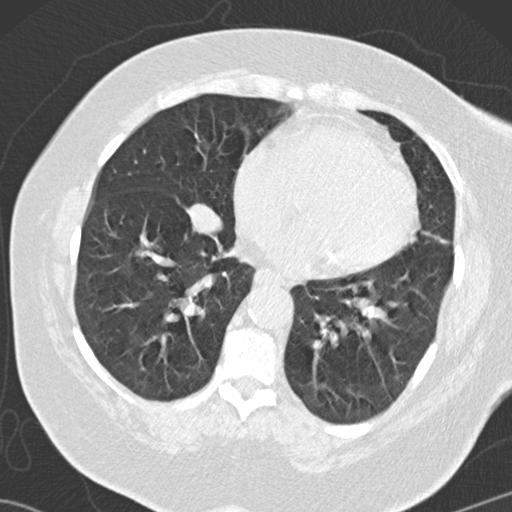
Low-dose screening chest CT, one axial slice; position 53 of 146 along the scan axis; 120 kVp; lung window (W 1500 / L -600 HU); 512 × 512 image matrix, field of view 350 × 350 mm.
Outlined on this slice (manually delineated by an expert):
- lesion 3 (tumor, lower lobe of right lung): bounding box (x1, y1, x2, y2) in pixels: (192, 205, 221, 233)